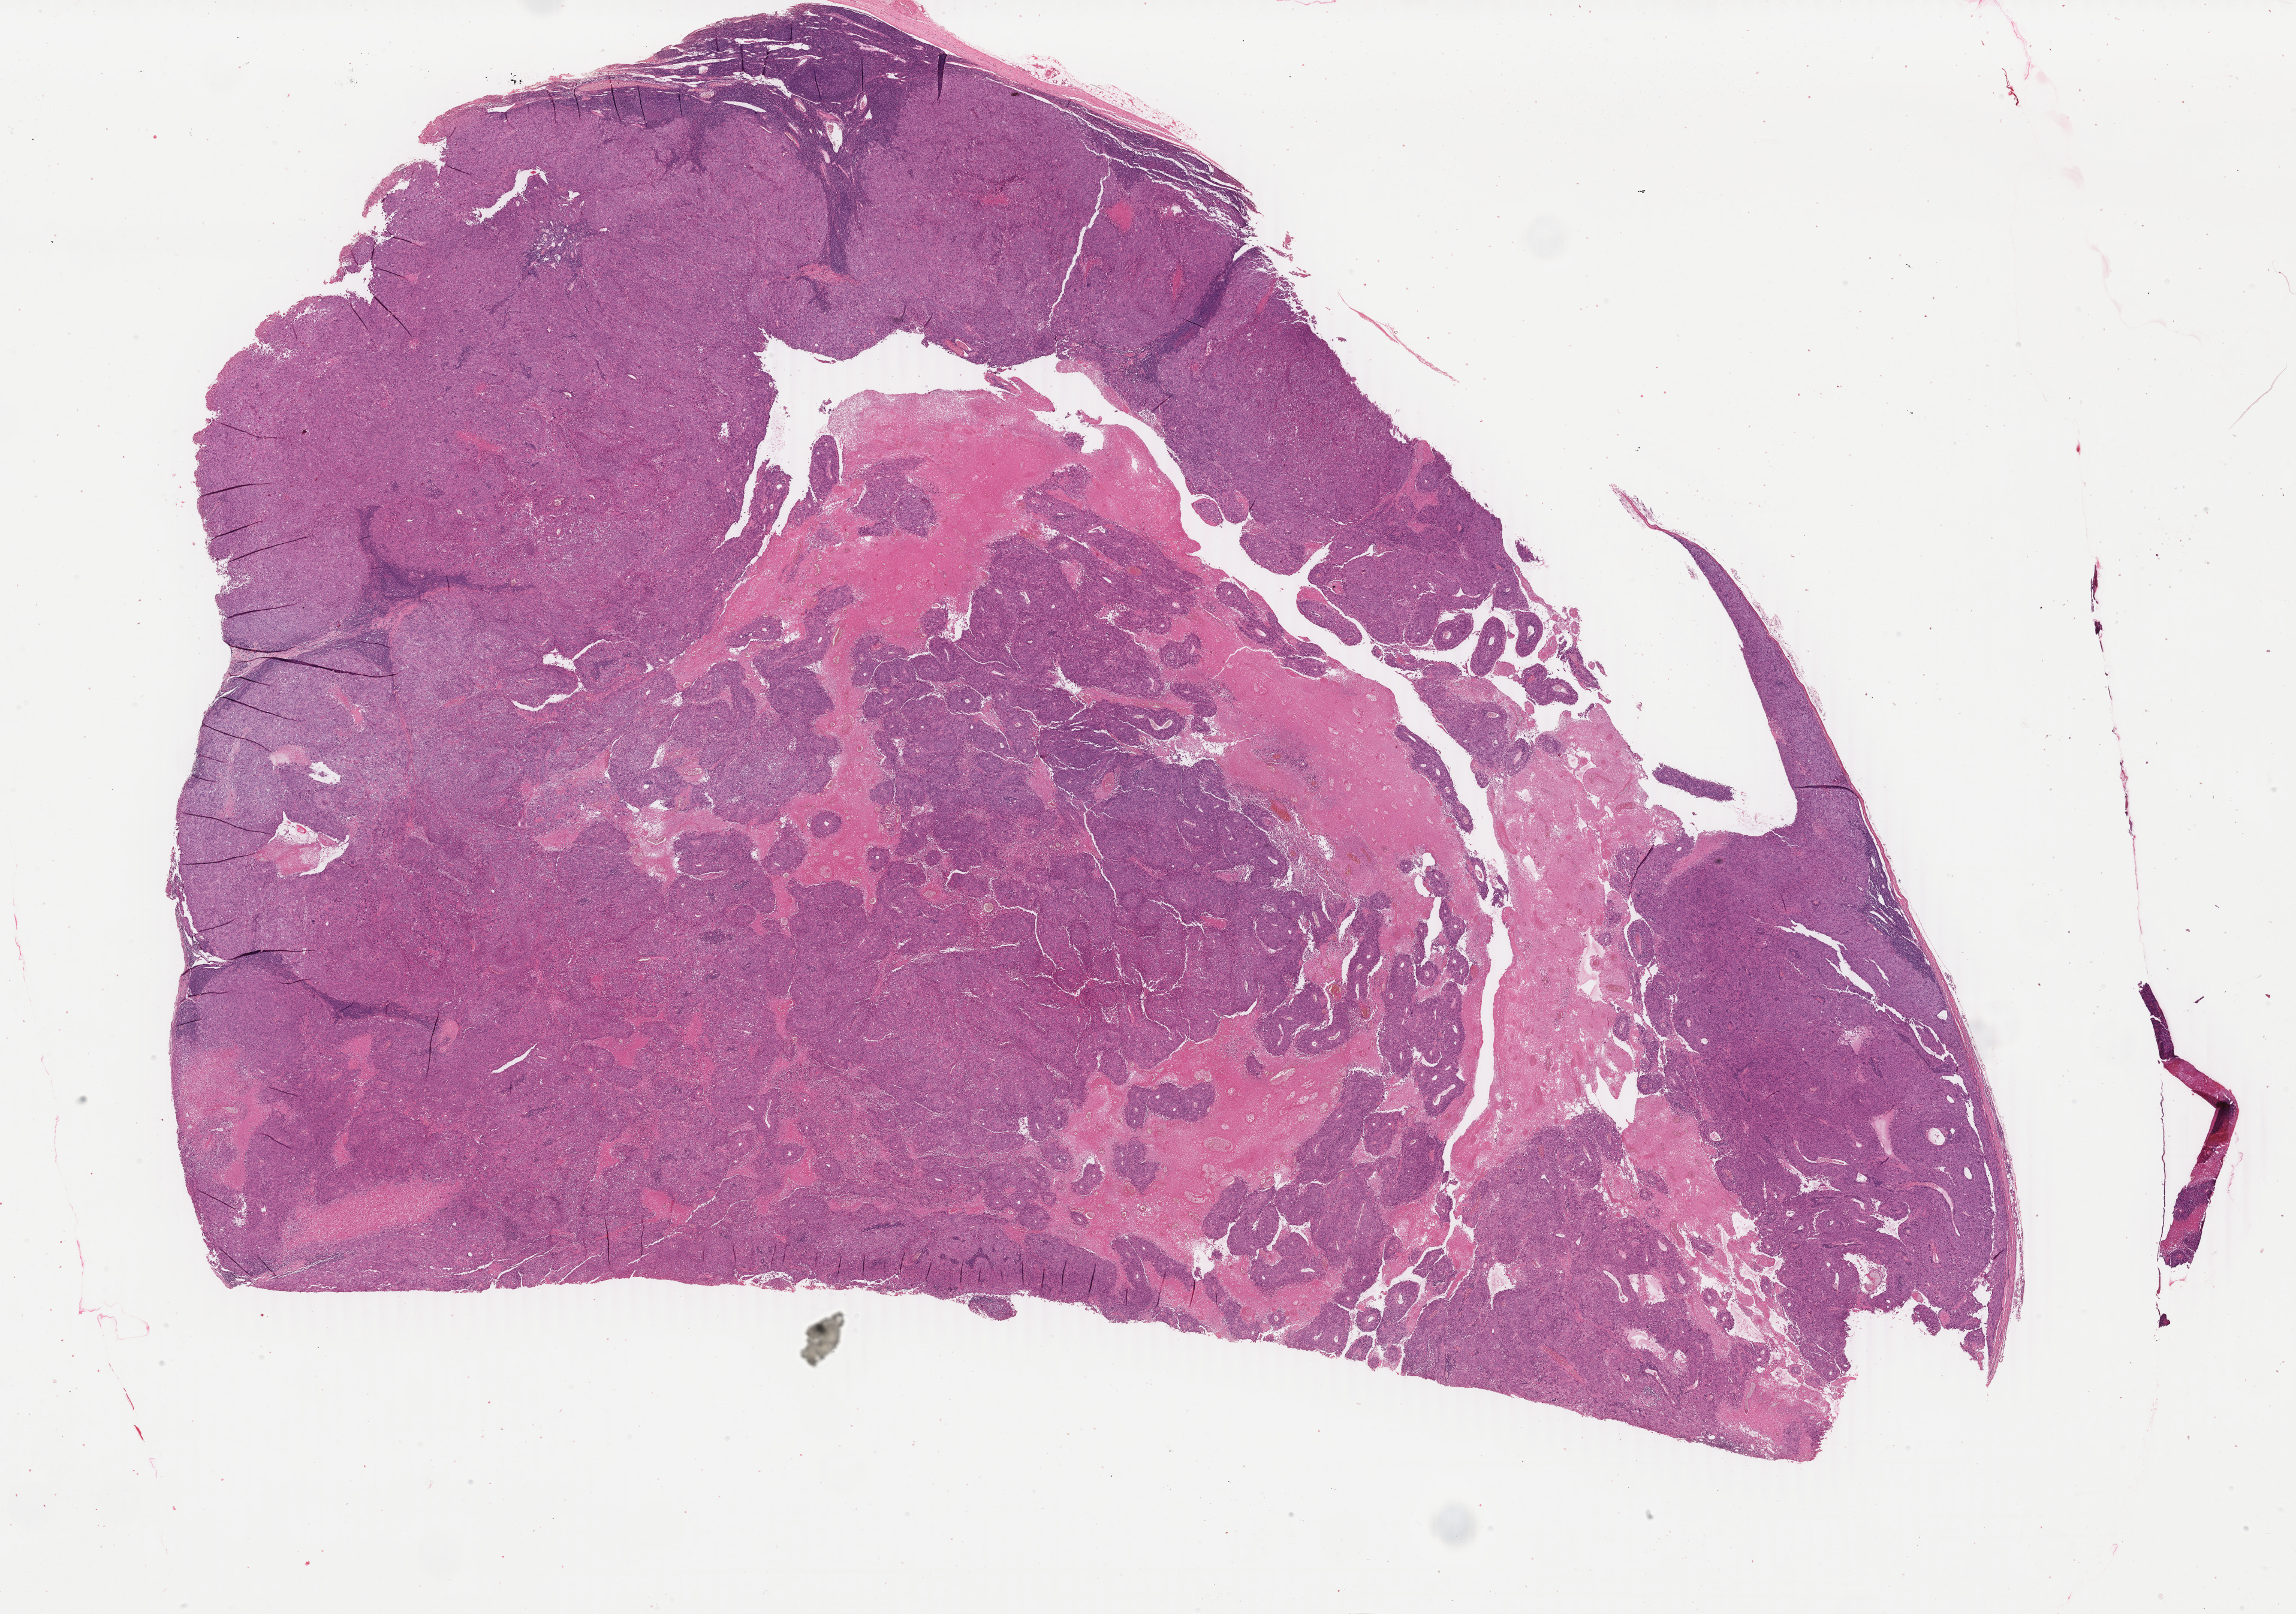
H&E-stained whole-slide image — shown as a low-resolution overview of the whole scanned area (about 30.5 x 21.4 mm, acquisition: 40x scan), FFPE section, primary tumour sample from the skin. Female, age 33 years at initial diagnosis.
Histologic diagnosis: Malignant melanoma, NOS.